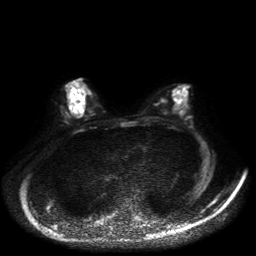
Breast MRI, one axial slice. Position 22 of 50 along the scan axis. Diffusion-weighted series; image 2 of 4 stored at this slice position (different b-values; order by instance number). 1.5 T. 4 mm slice thickness. 256 × 256 image matrix. Female patient.
Outlined on this slice (expert manual segmentation):
- tumour on diffusion-weighted imaging: box from (x=76, y=103) to (x=82, y=107) px